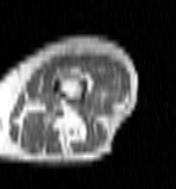
MRI of an extremity soft-tissue mass, one axial slice; slice 27 of 100 in the series (ordered by position); MR volume resampled by the dataset authors to the PET/CT grid (not the native acquisition matrix); 3.27 mm slice thickness; 176 × 189 image matrix. Female patient. From the clinical record (not read from this slice): histological type: undifferentiated – high grade; grade: high; site of the primary tumour: left thigh.
Structures marked on this image (expert contour drawn on MRI and transferred to this co-registered scan by the dataset authors):
- gross tumour volume including surrounding oedema: bounding box [x1, y1, x2, y2] px = [67, 61, 120, 104]